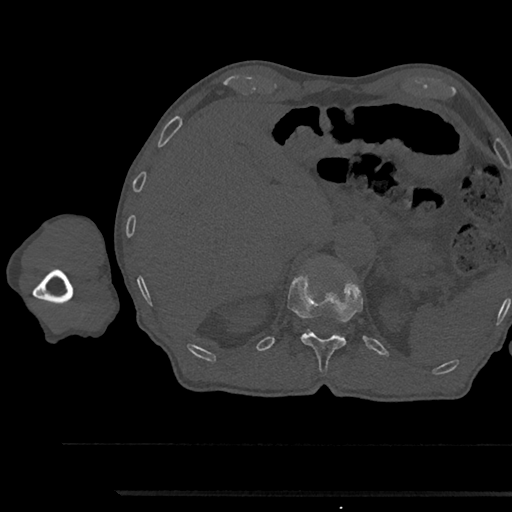
CT including the spine, one axial slice. Slice 701 of 797 in the series (ordered by position). Bone window (W 1800 / L 400 HU). 0.5 mm slice thickness. 512 × 512 image matrix, field of view 367 × 367 mm. Patient: male, 79 years. From the clinical record (not read from this slice): primary cancer: prostate.
Annotated regions visible in this slice (semi-automatic segmentation, software-assisted and operator-edited):
- T12 vertebra: bounding box (x1, y1, x2, y2) in pixels: (288, 276, 362, 372)